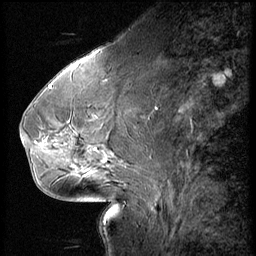
Breast MRI (dynamic contrast-enhanced), one sagittal slice. Slice 27 of 66 in the series (ordered by position). 3 images stored at this slice position (order not interpretable as contrast timing). 1.5 T. TE 4.2 ms, TR 8.9 ms. 2.5 mm slice thickness. 256 × 256 image matrix, field of view 200 × 200 mm. Female patient, age 54 years. Case-level facts recorded for this patient, not image findings: setting: breast cancer imaged before/during neoadjuvant chemotherapy; receptor status: HR-positive, HER2-negative.
Annotated regions visible in this slice (semi-automatically segmented with operator editing):
- analysis volume of interest (the breast-tissue region the enhancement analysis was run in; not a lesion): bounding box (x1, y1, x2, y2) in pixels: (61, 104, 146, 171)
- tumour enhancement mask (voxels above the 140 % enhancement threshold inside the analysis volume of interest): (95, 148, 97, 151)